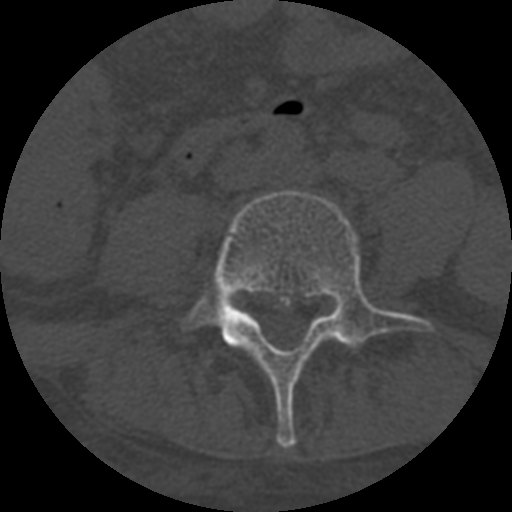
CT including the spine, one axial slice; slice 208 of 708 in the series (ordered by position); one of 3 acquisitions stored at this slice position; bone window (W 1800 / L 400 HU); 1.25 mm slice thickness; 512 × 512 image matrix, field of view 160 × 160 mm. Patient age 55 years. Case-level facts recorded for this patient, not image findings: primary cancer: colon; vertebrae with lytic lesions (as recorded): T12, L1, L5.
Annotated regions visible in this slice (semi-automatically segmented with operator editing):
- L4 vertebra: box from (x=177, y=190) to (x=434, y=448) px